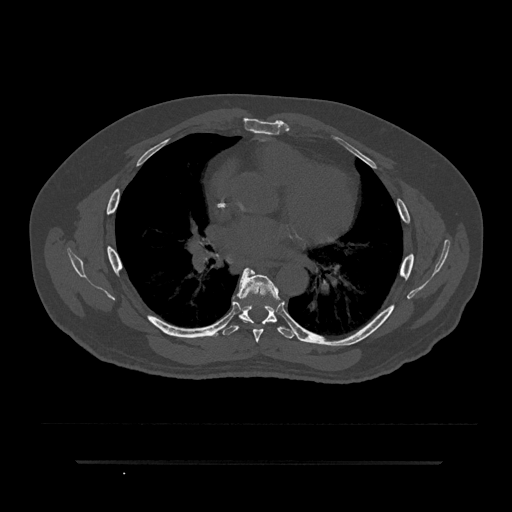
CT including the spine, one axial slice. Position 504 of 797 along the scan axis. 120 kVp. Bone window (W 1800 / L 400 HU). 0.5 mm slice thickness. 512 × 512 image matrix. Male patient, age 59 years. From the clinical record (not read from this slice): primary cancer: bile ducts; vertebrae with lytic lesions (as recorded): T10.
Outlined on this slice (semi-automatically segmented with operator editing):
- T6 vertebra: bounding box <236,268,280,343> (left, top, right, bottom; pixels)
- T7 vertebra: <222,270,295,339>